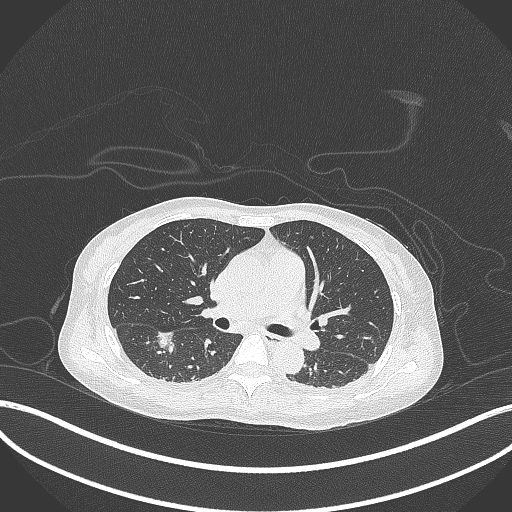
Chest CT, one axial slice; position 180 of 261 along the scan axis; 120 kVp; lung window (W 1500 / L -600 HU); 1 mm slice thickness; 512 × 512 image matrix. Female patient, age 44 years. Case-level facts recorded for this patient, not image findings: clinical TNM (as recorded): T1c N0 M0.
Outlined on this slice (bounding box drawn by a radiologist):
- lung tumour (recorded histology: adenocarcinoma): box from (x=152, y=328) to (x=176, y=353) px